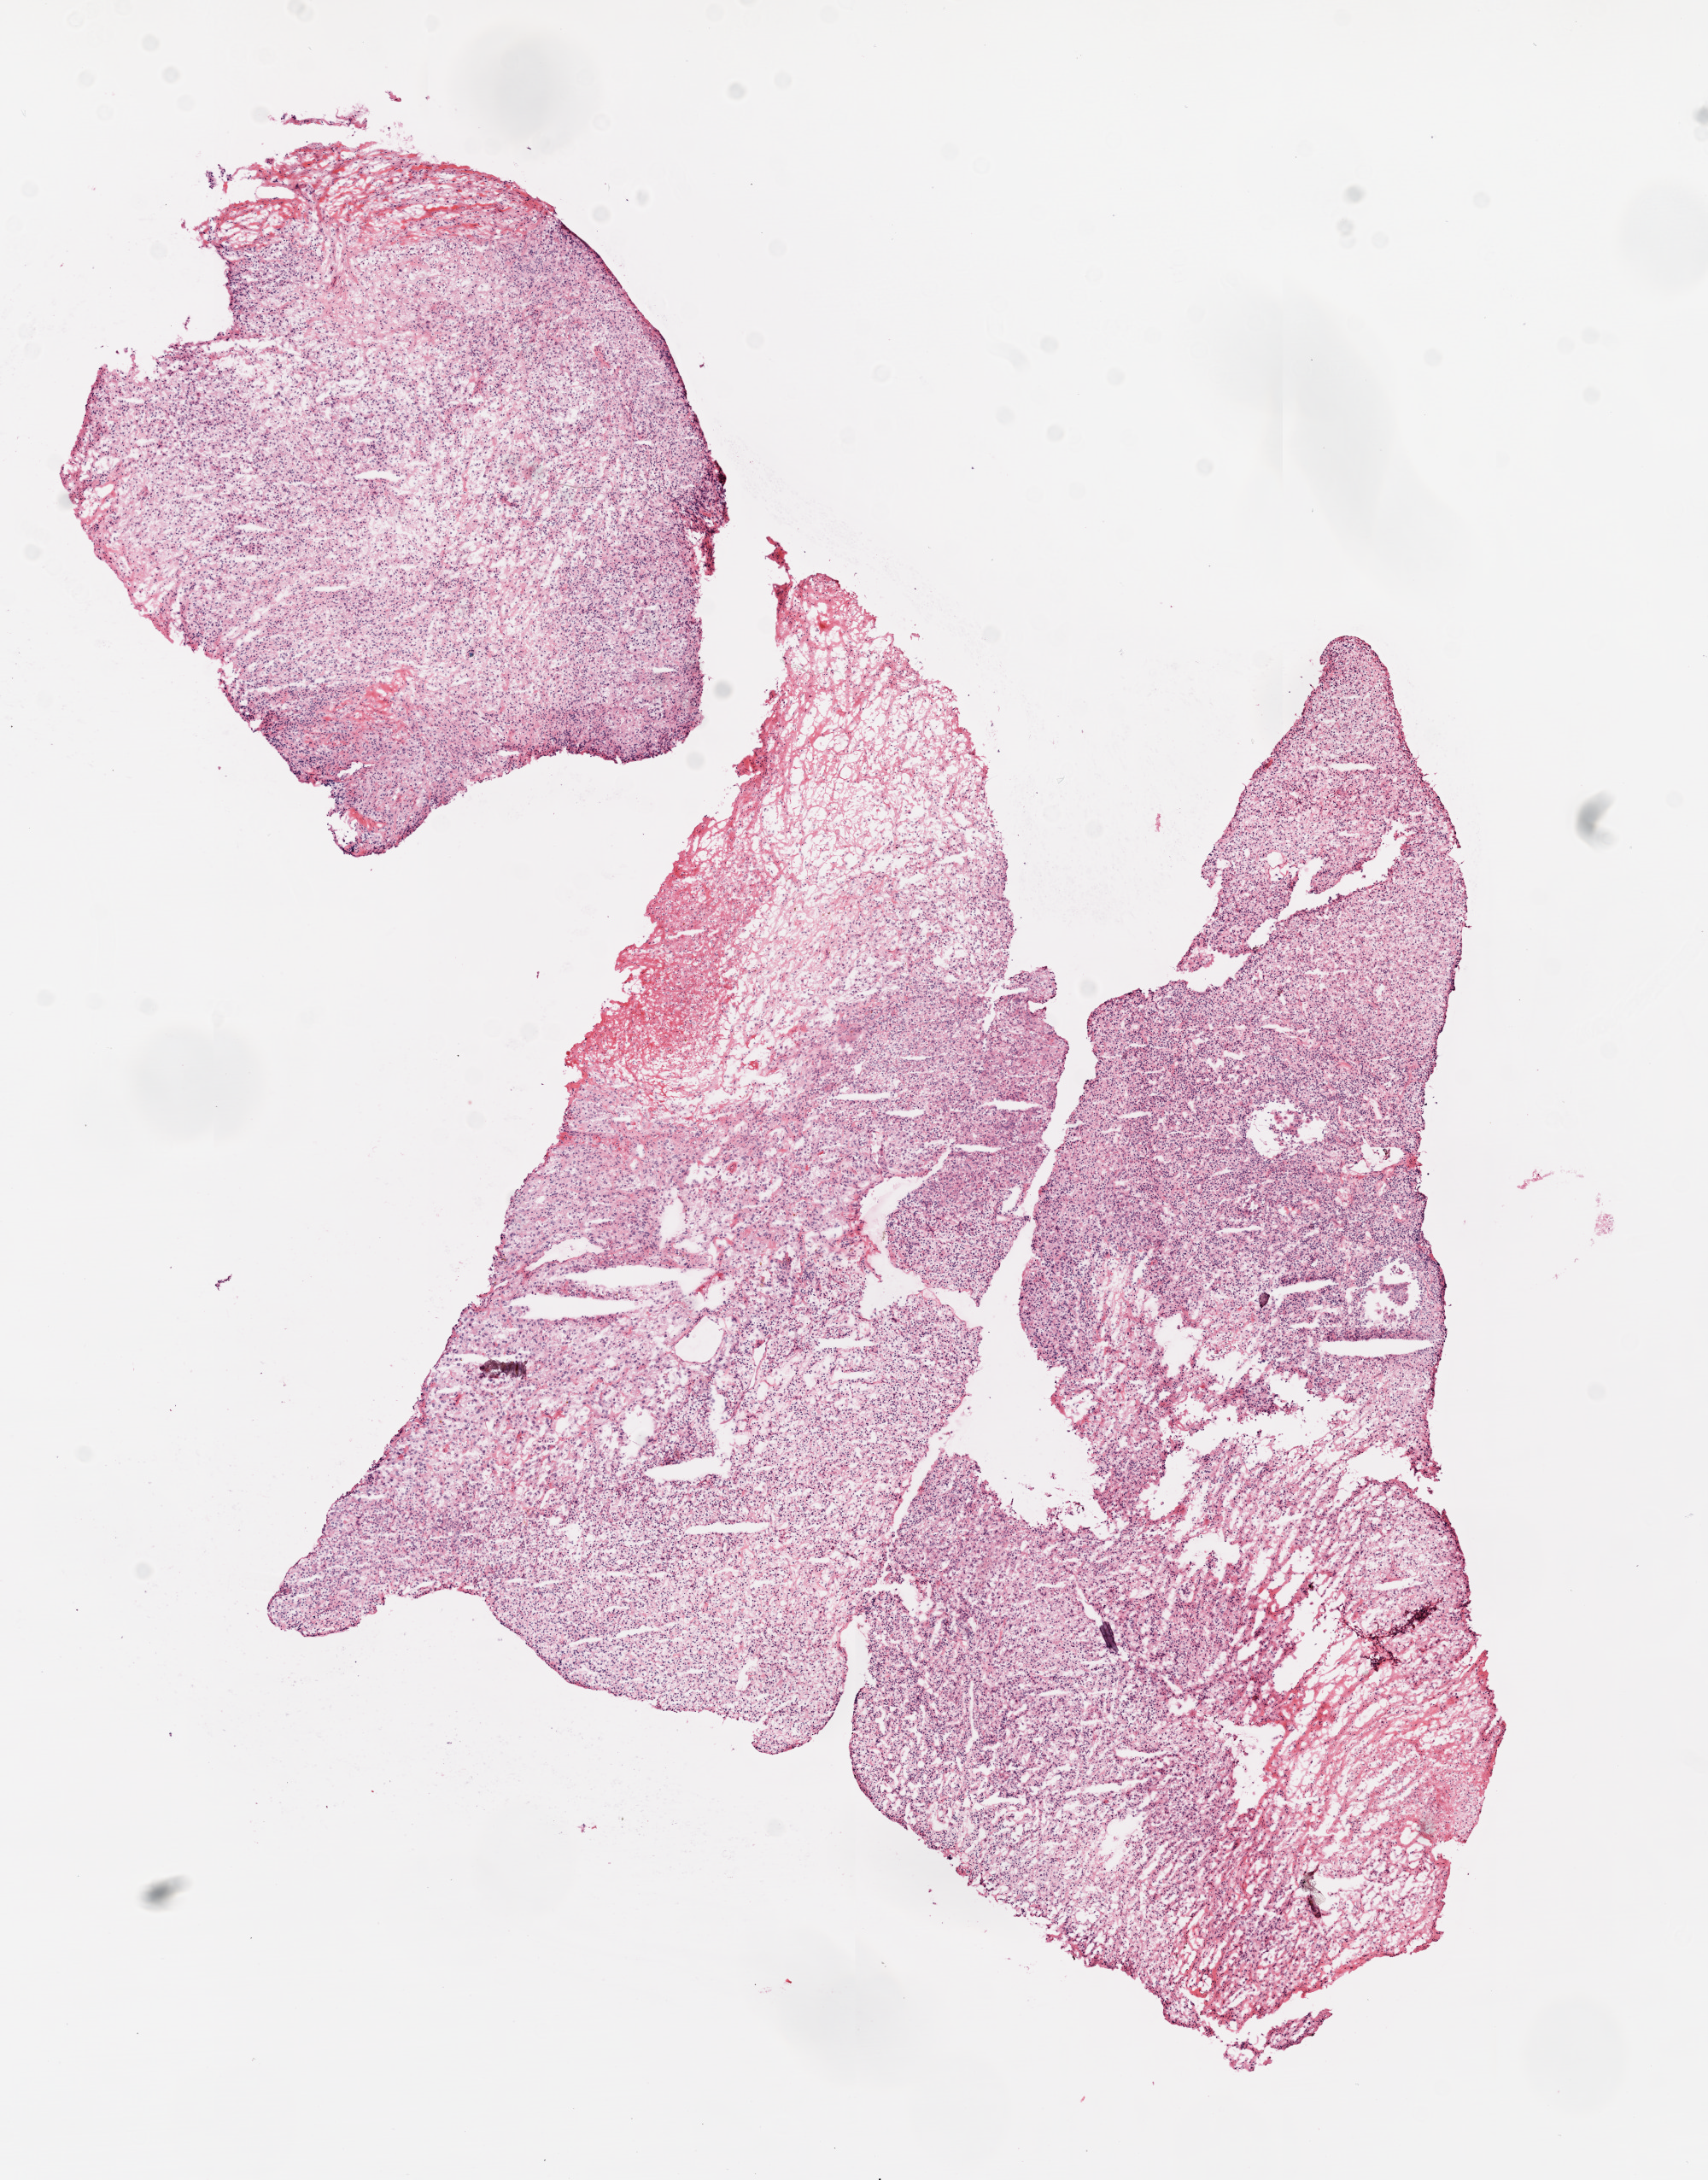
Whole-slide histology image, H&E-stained, whole scanned area (about 8.0 x 10.2 mm, from a 20x scan) shown as a low-resolution overview. Frozen section from the top of the tissue portion. Kidney, primary tumour sample. Male patient; age at initial diagnosis 63 years. Pathologist review of this section (percent, as recorded): tumour cells 85%, tumour nuclei 85%.
Histologic diagnosis: Clear cell adenocarcinoma, NOS.